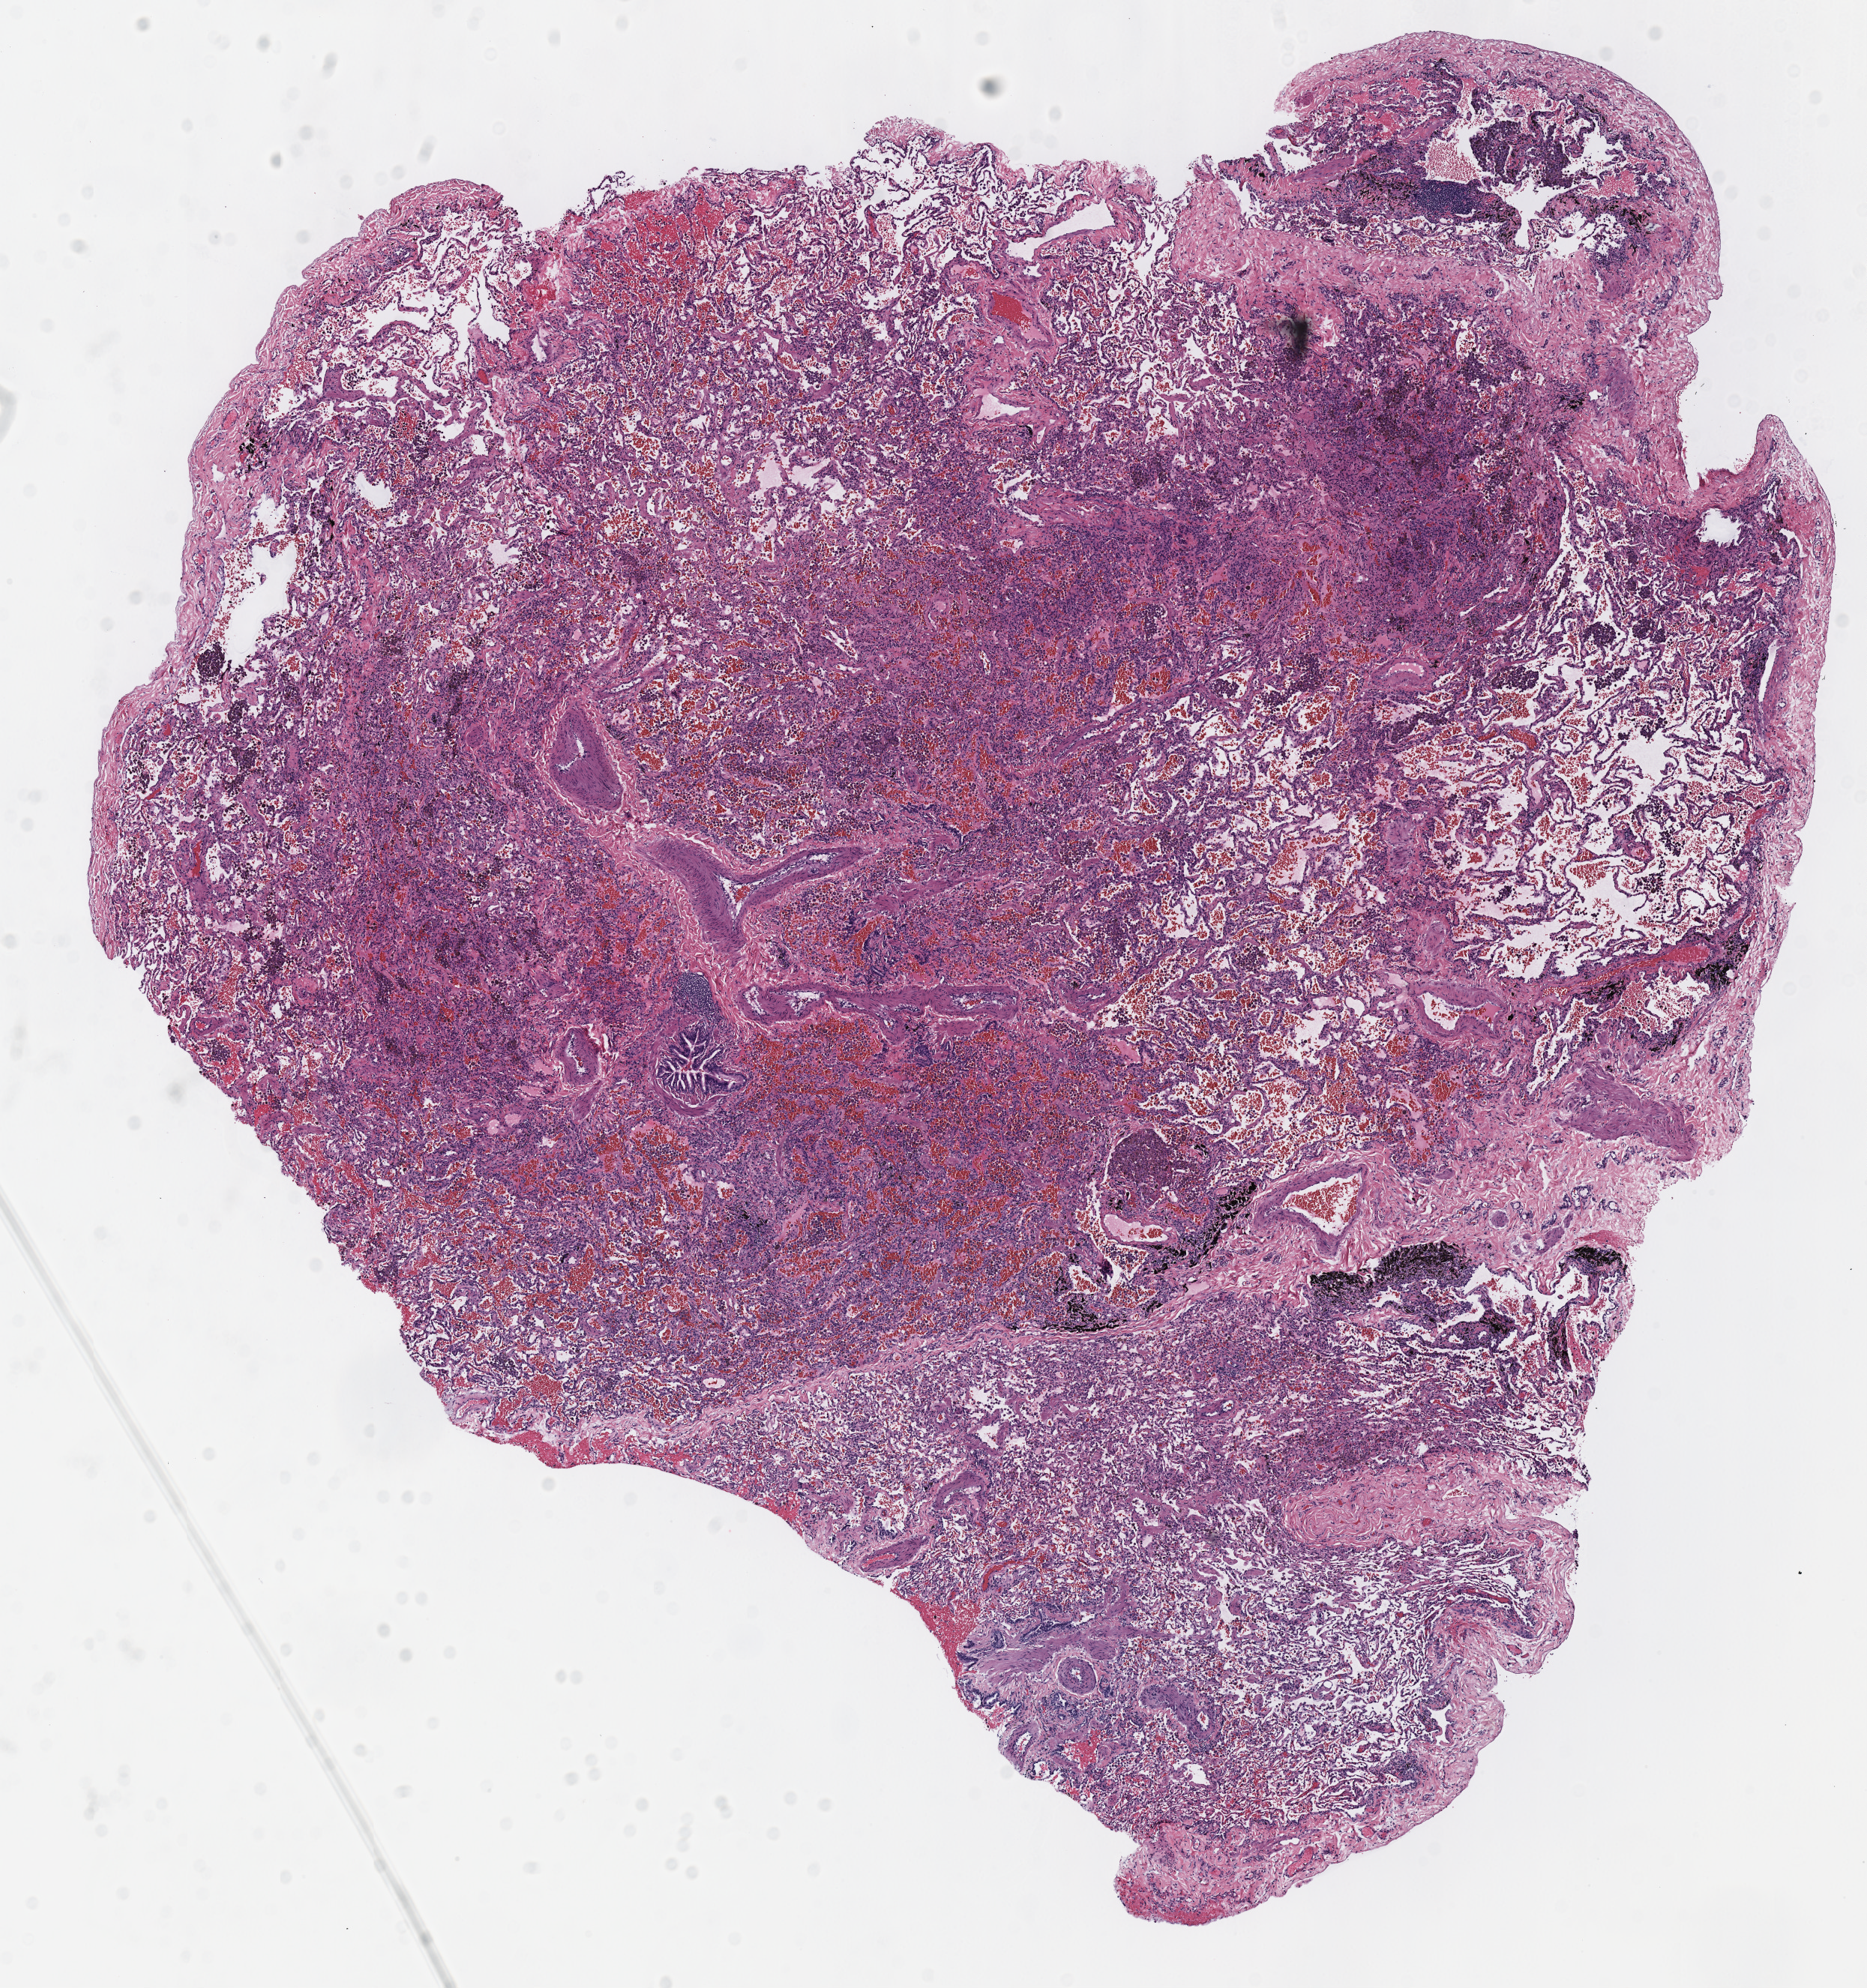
Digitized H&E tissue section (whole slide) — whole scanned area (about 9.8 x 10.4 mm) shown as a low-resolution overview. Frozen section from the top of the tissue portion. Solid tissue normal (non-tumour tissue) sample from the lung. Patient: male, age at initial diagnosis 59 years.
This section: solid tissue normal (non-tumour) sample from the same patient. Patient diagnosis: Adenocarcinoma, NOS (upper lobe, lung).